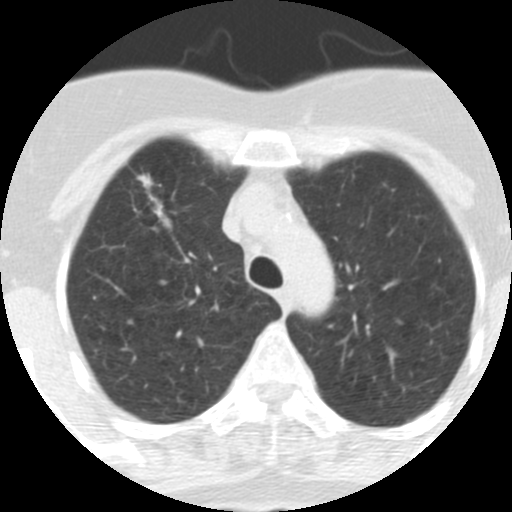
Axial slice from a low-dose chest CT screening exam; baseline annual screen; lung window (W 1500 / L -600 HU); 2.5 mm slice thickness; standard (soft-tissue) reconstruction kernel (STANDARD); 120 kVp; slice 68 of 313 in the series. Female, age 62 years at enrolment.
Expert-annotated lung lesion, box from (x=116, y=165) to (x=186, y=235) px. Reader record for this screening exam (exam-level; its link to the box is not recorded): non-calcified nodule or mass ≥4 mm, right upper lobe, 9 × 7 mm, spiculated (stellate) margins, soft tissue attenuation.